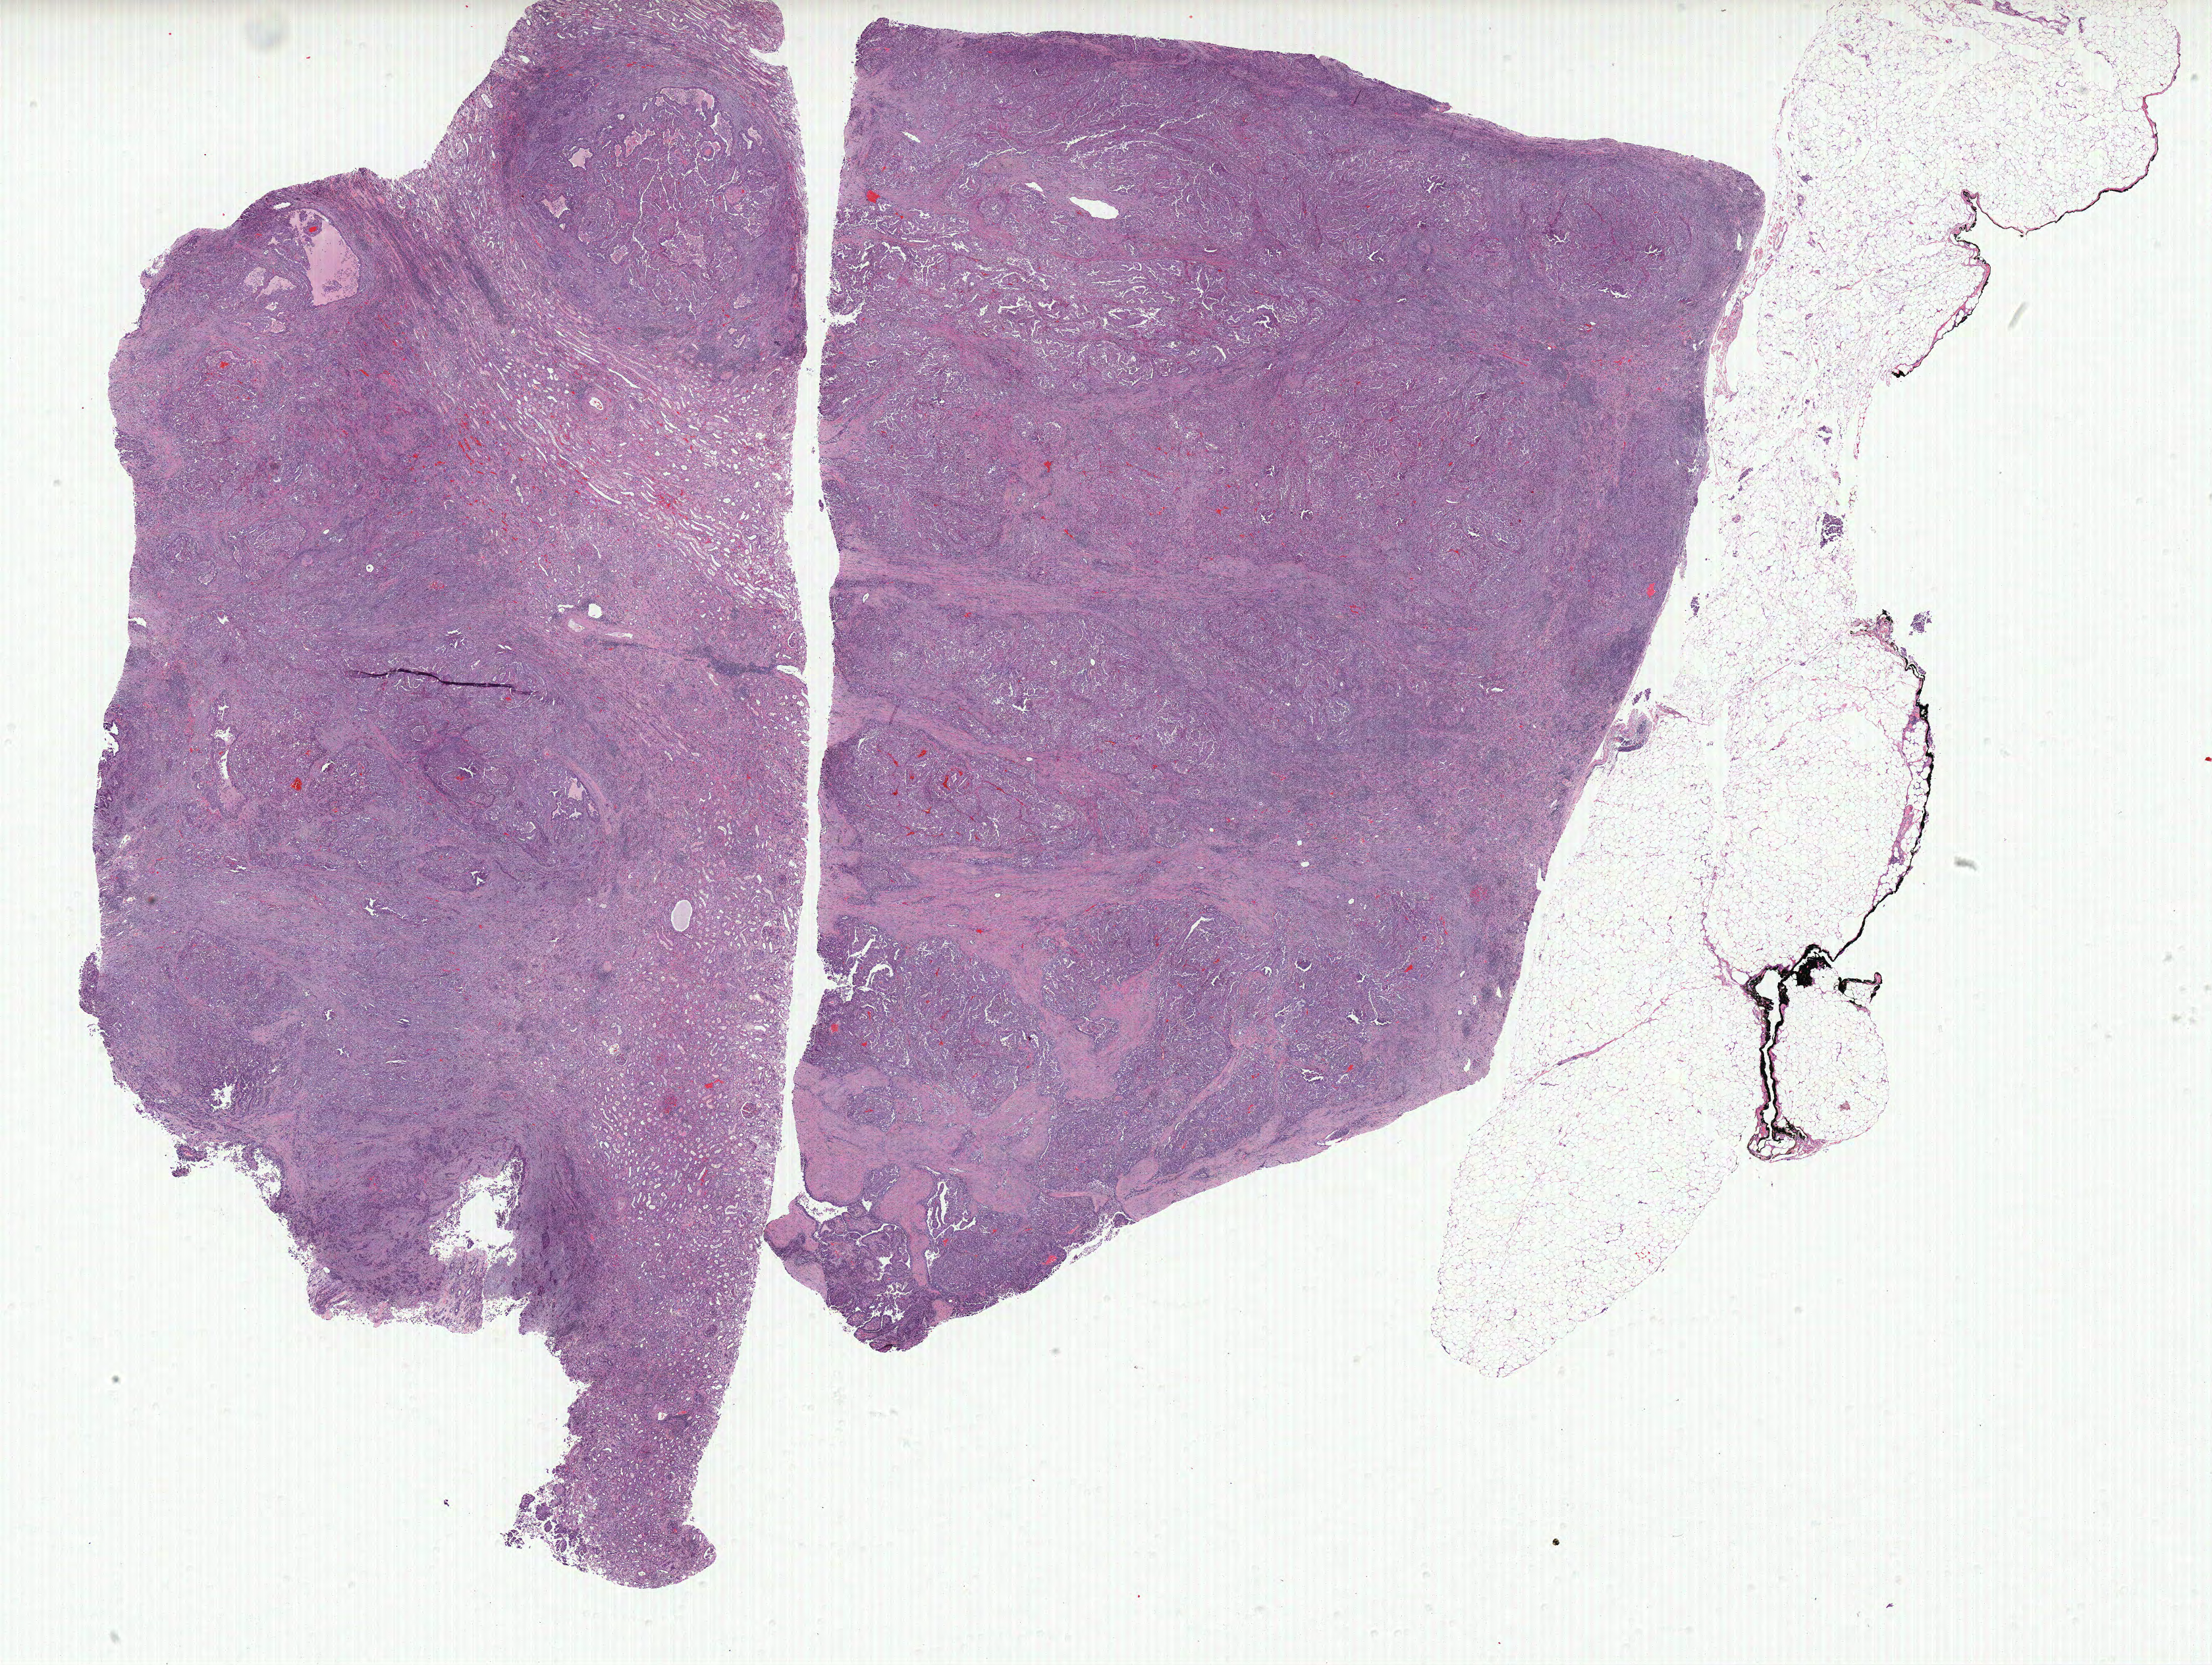
Whole-slide histology image, H&E — low-resolution overview of the scanned area, about 26.9 x 20.2 mm (acquisition: 40x scan). Formalin-fixed paraffin-embedded (FFPE) diagnostic section. Primary tumour sample from the kidney. Patient: male, age at initial diagnosis 42 years.
Lymph nodes positive (case pathology): 11 of 17 examined. Histologic diagnosis: Papillary adenocarcinoma, NOS. AJCC pathologic stage: IV.